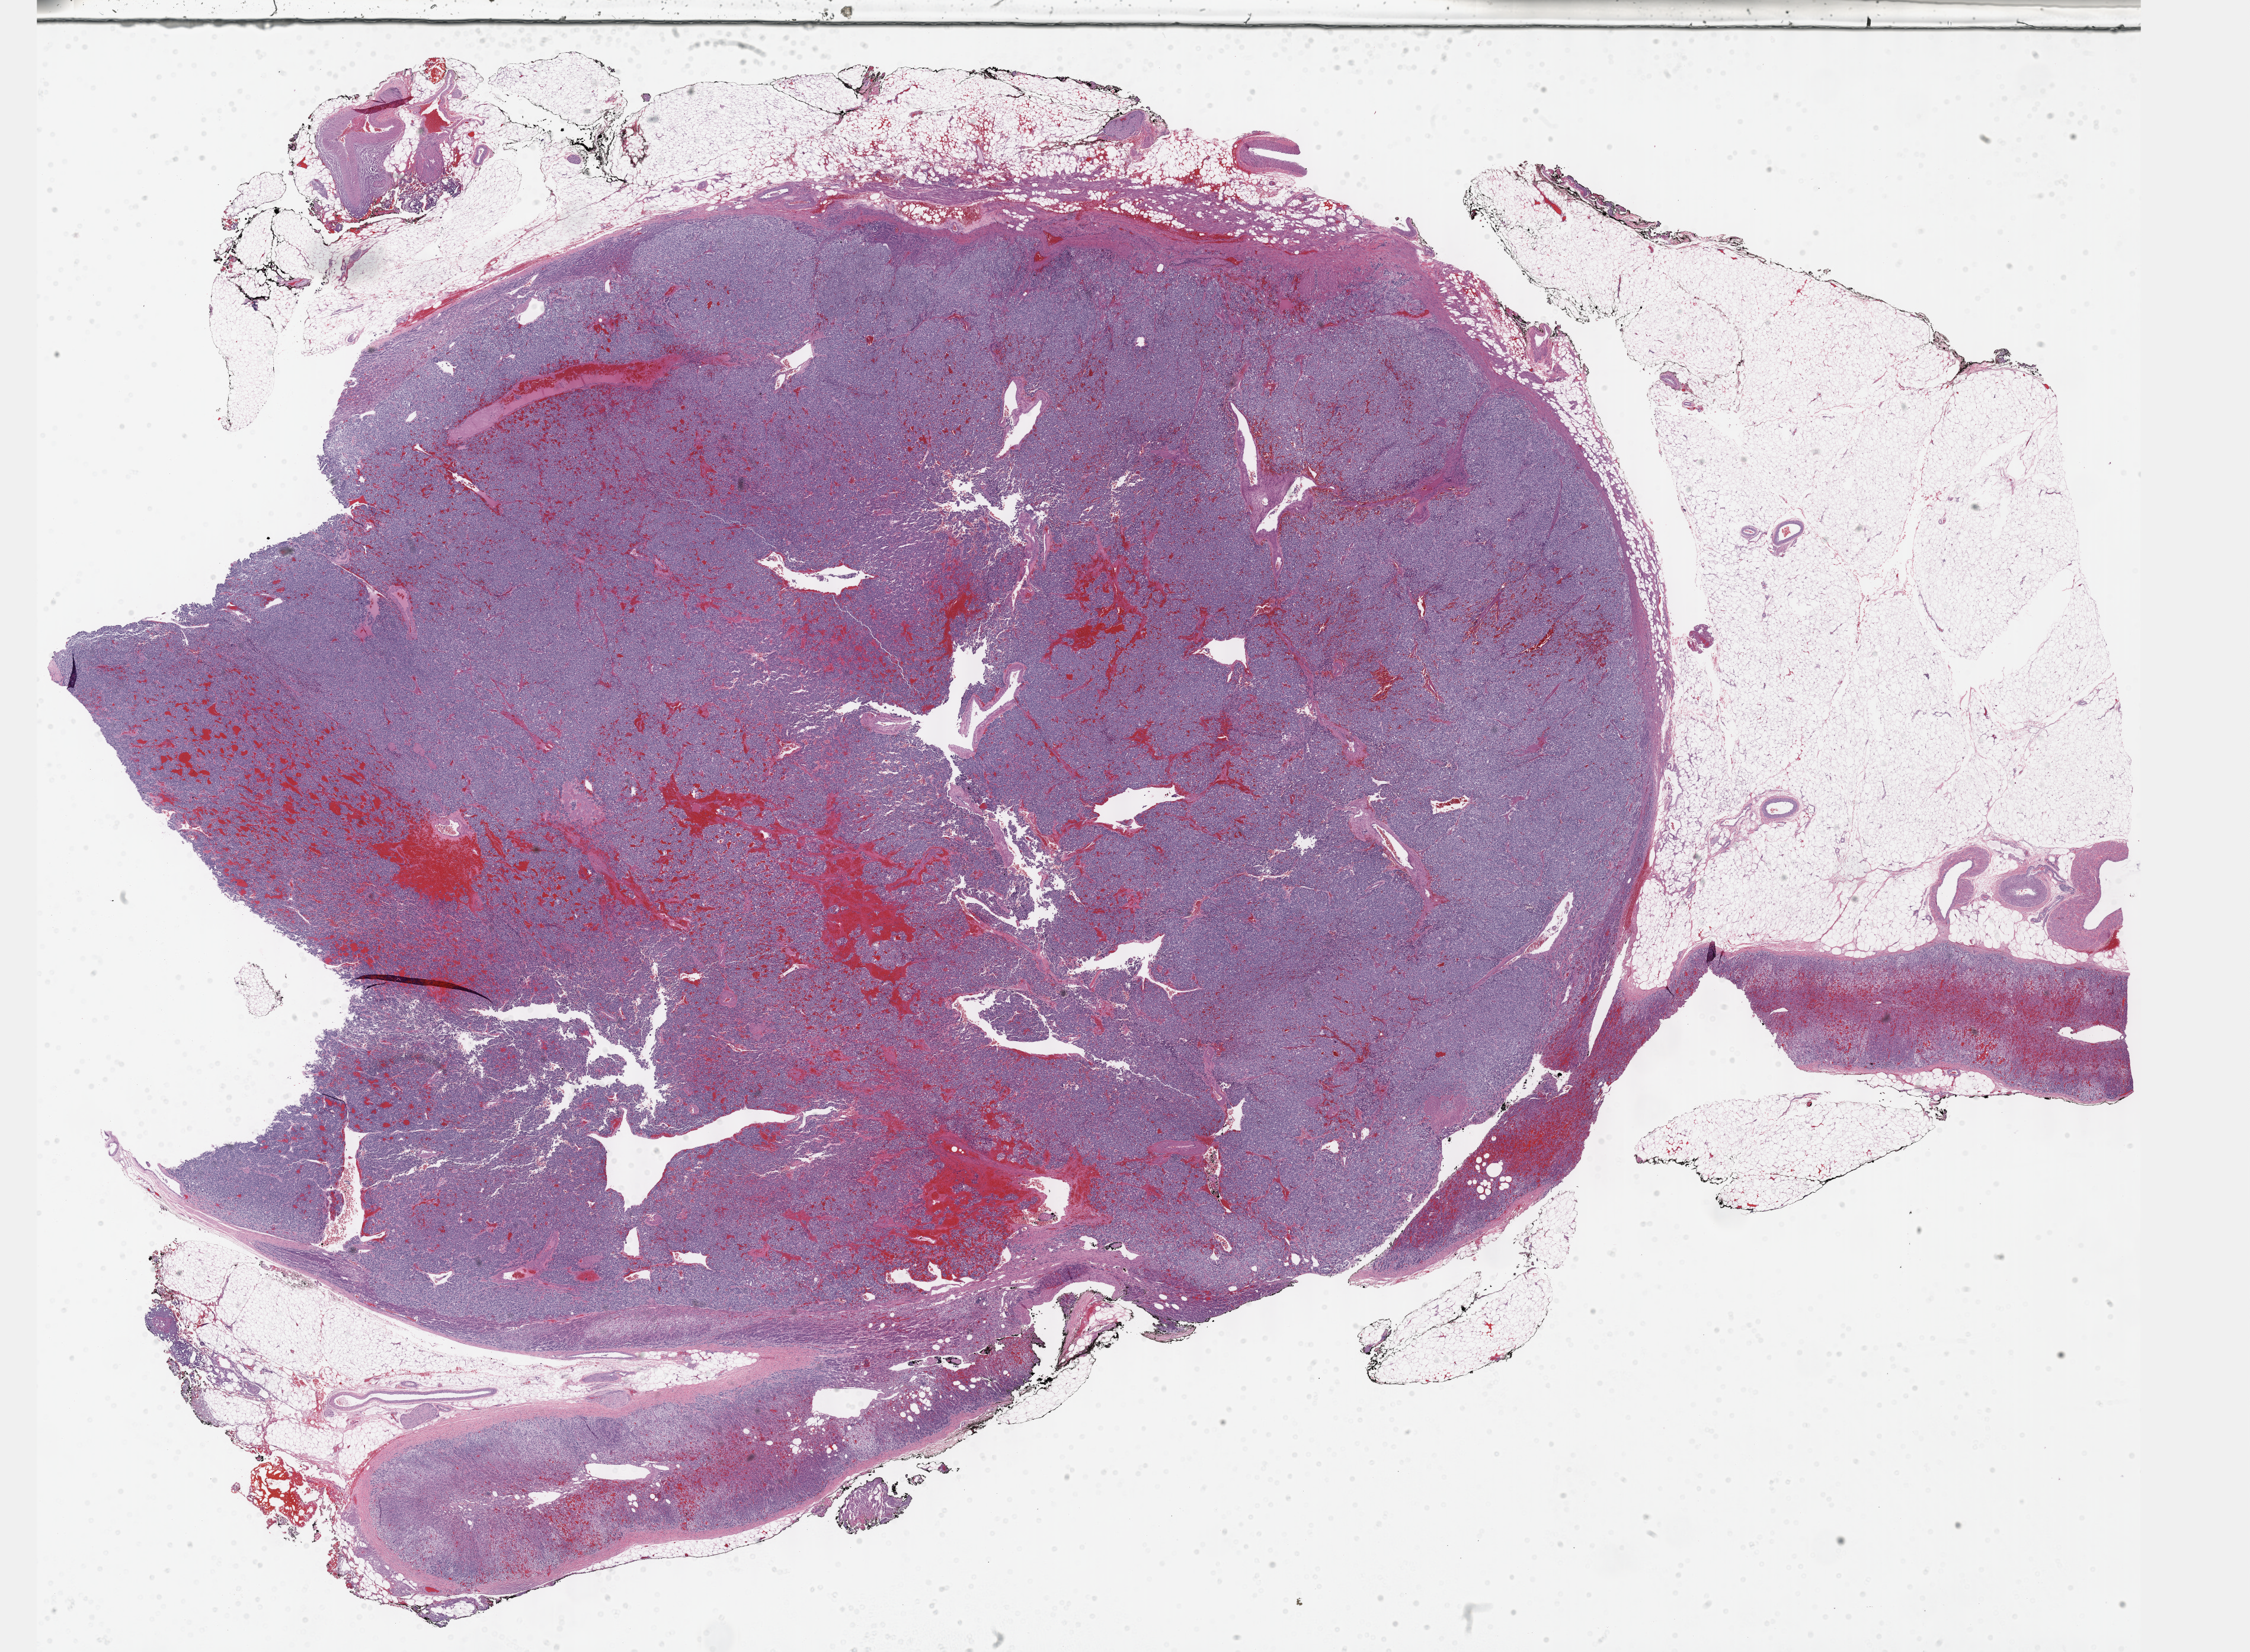
H&E whole-slide image, low-resolution overview of the scanned area, about 30.7 x 22.5 mm; formalin-fixed paraffin-embedded (FFPE) diagnostic section; sample: primary tumour, adrenal gland. Female, age 45 years at initial diagnosis.
- histologic diagnosis: Pheochromocytoma, NOS